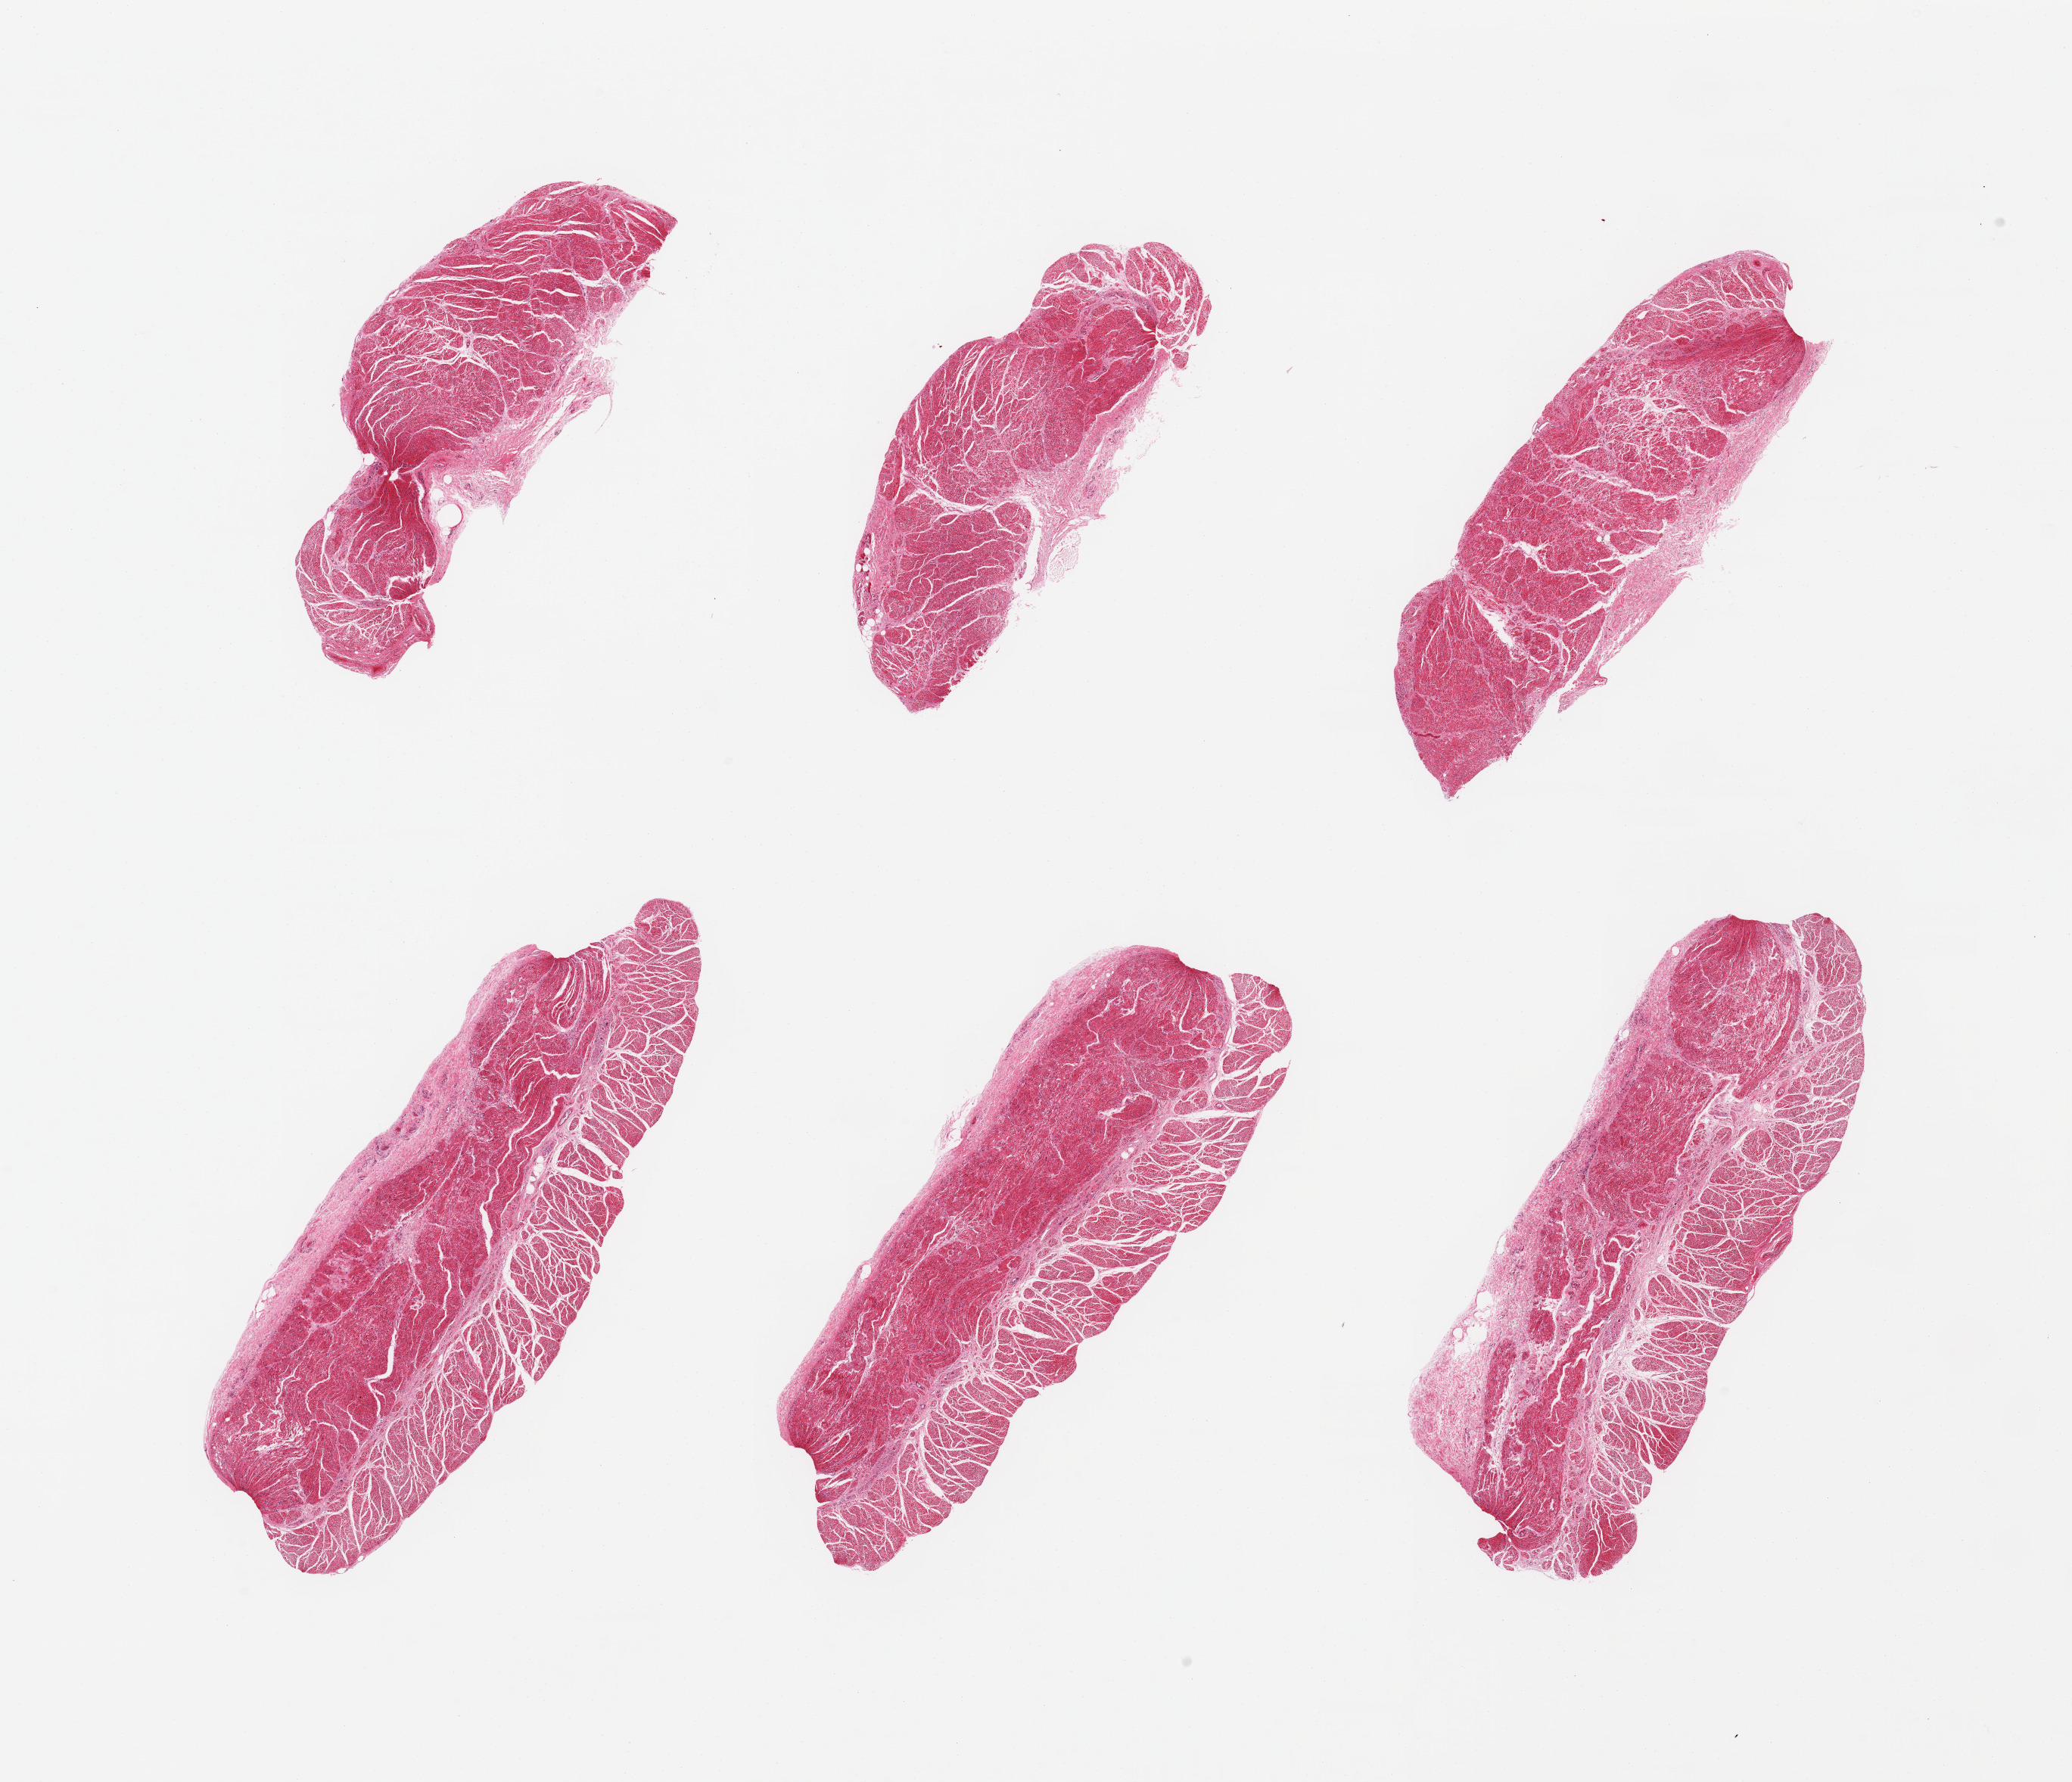
Whole-slide image, haematoxylin and eosin stain, a low-resolution overview of the entire scanned area, about 21.7 x 18.6 mm. PAXgene-fixed paraffin-embedded (PFPE) section. Target tissue: gastroesophageal junction. Tissue donor sample. Donor sex: male.
Pathologist's review note for this sample: 6 pieces, confirmed target muscularis.